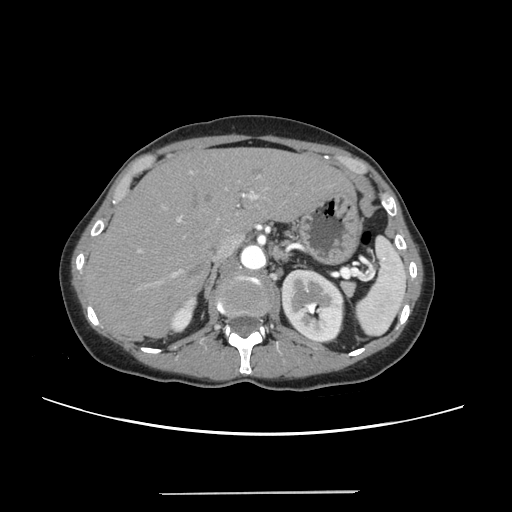
Contrast-enhanced abdominal CT, one axial slice; position 166 of 240 along the scan axis; 120 kVp; intravenous contrast given; soft-tissue window (W 400 / L 40 HU); 1.25 mm slice thickness; 512 × 512 image matrix, field of view 371 × 371 mm. Female patient, age 60 years. Case-level facts recorded for this patient, not image findings: diagnosis: colorectal cancer liver metastases, imaged before liver resection; multiple liver metastases: no; largest metastasis: 1.5 cm; disease in both lobes: no.
Structures marked on this image (manually delineated by an expert):
- liver: bounding box <86,149,348,336> (left, top, right, bottom; pixels)
- planned liver remnant (the part of the liver to remain after resection): <86,149,348,336>
- portal vein (with intrahepatic branches): <138,172,260,302>